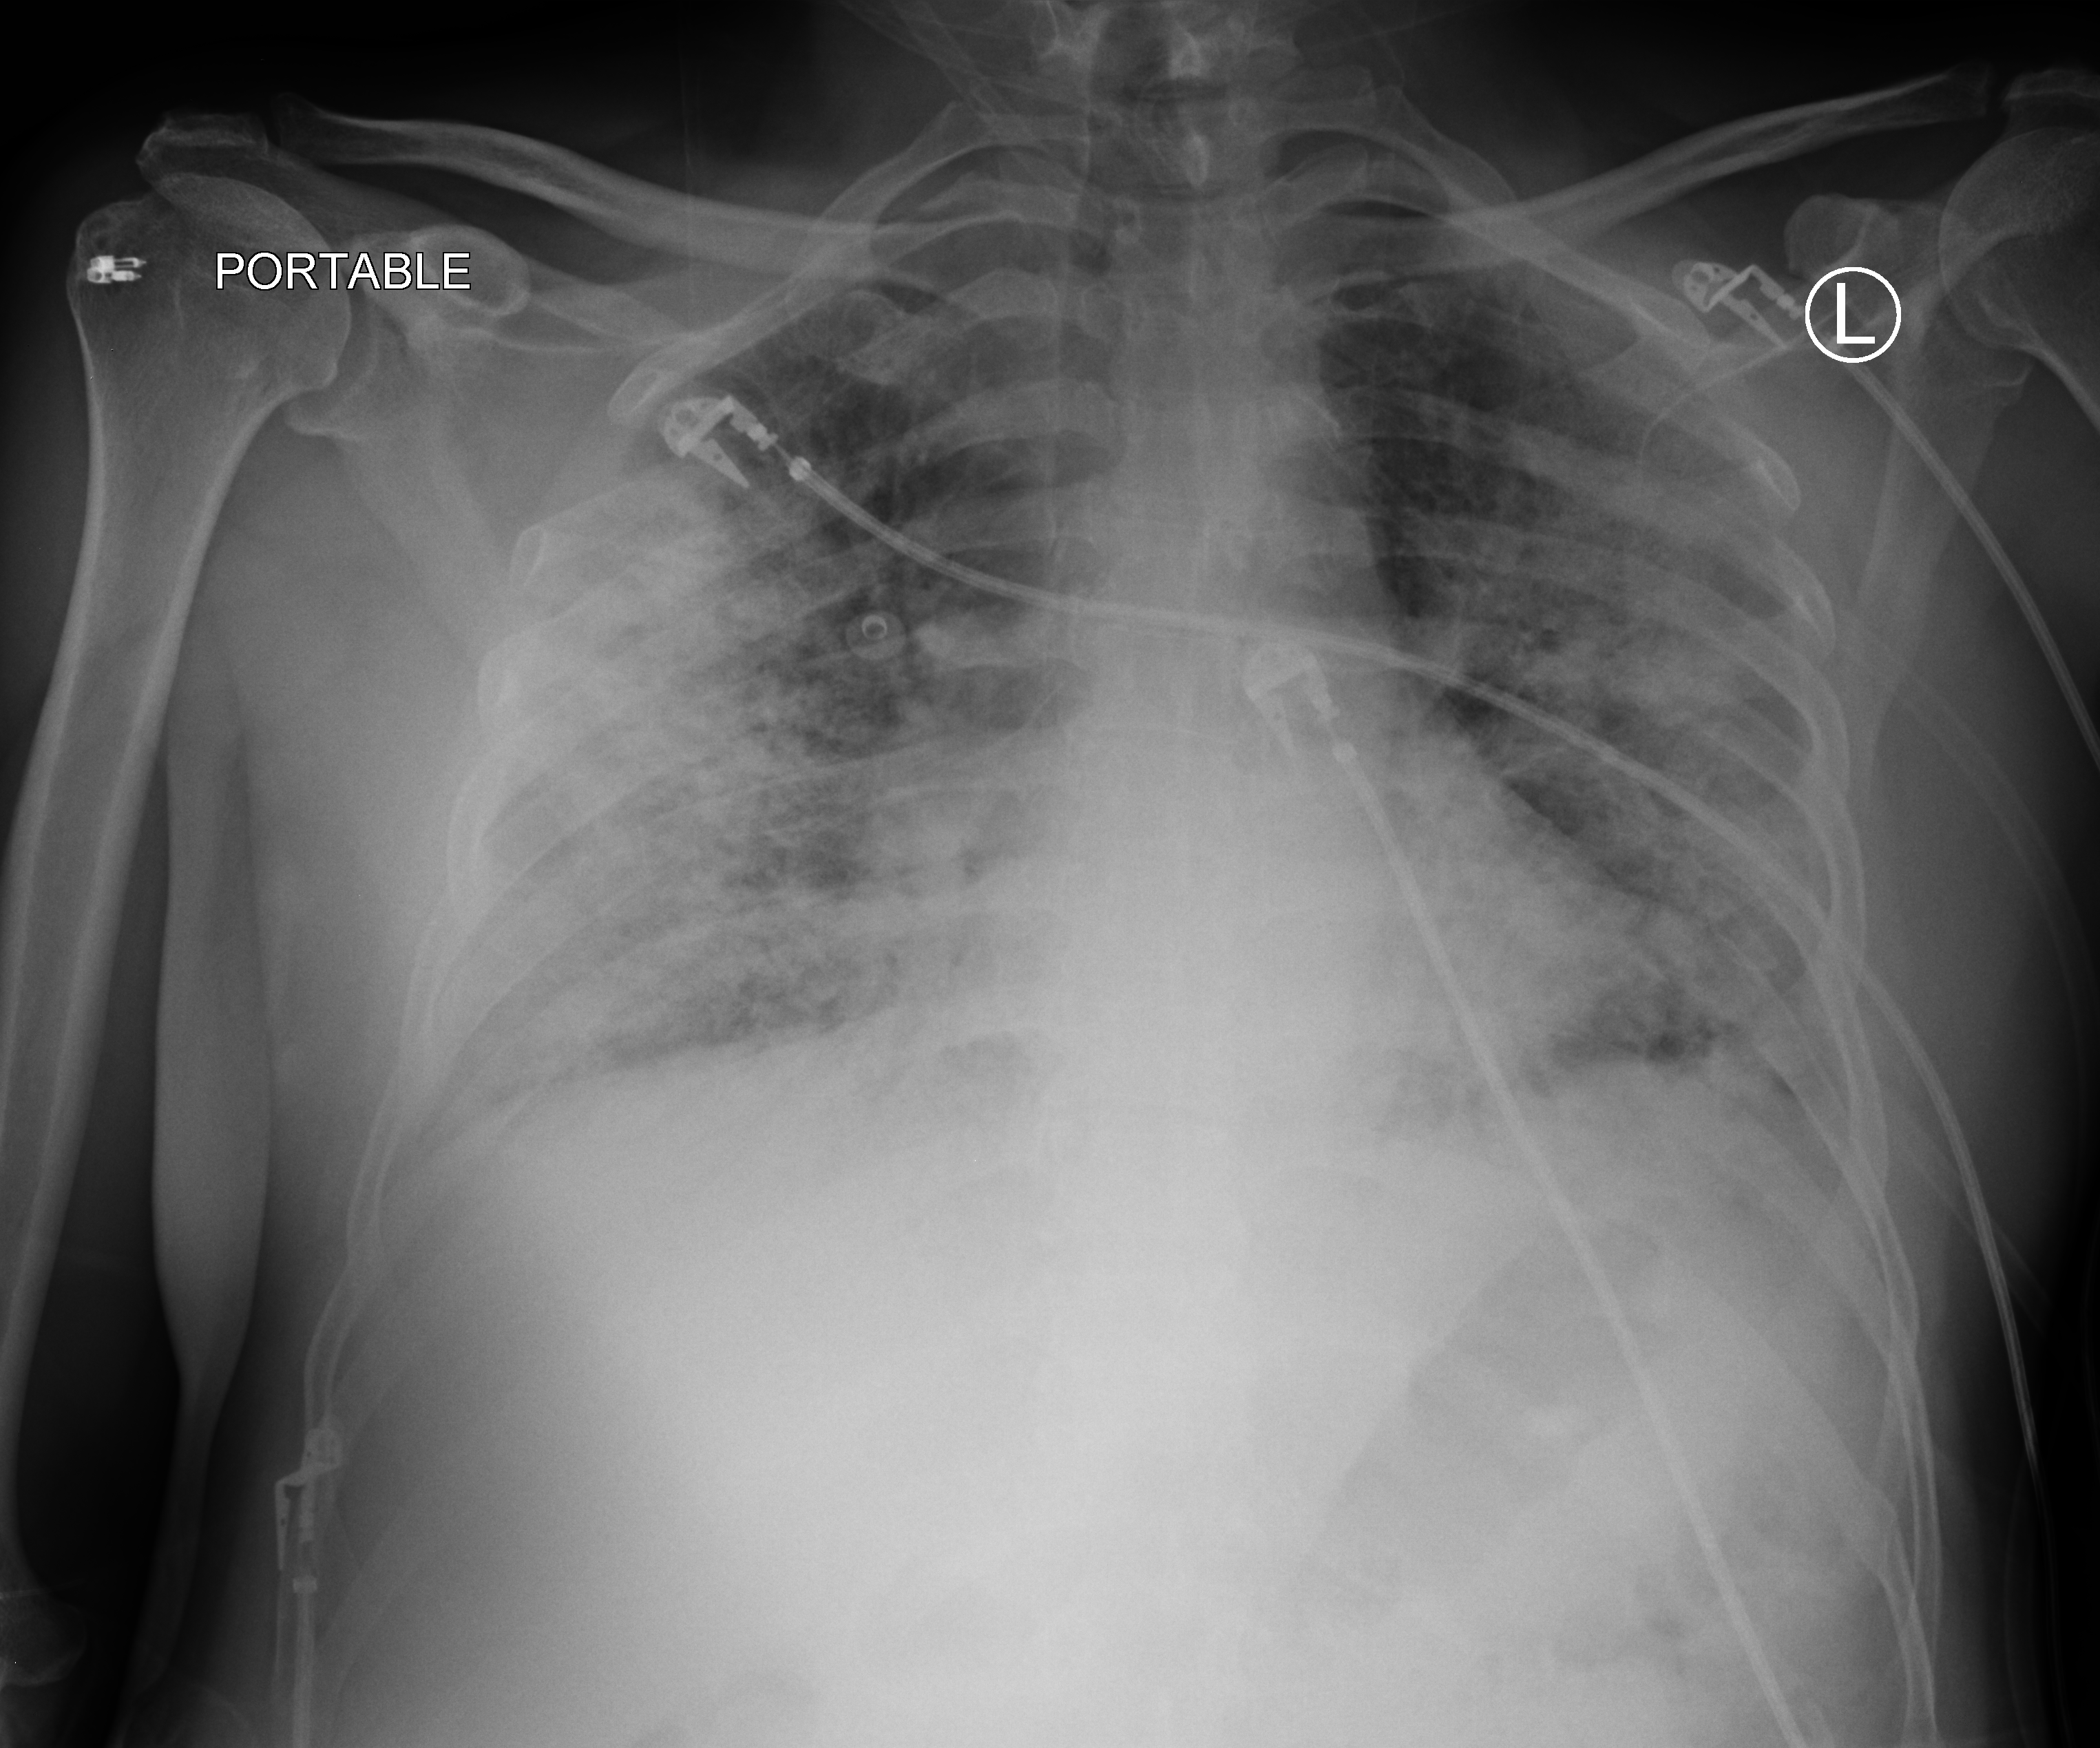
Portable chest radiograph; anteroposterior (AP) projection. Male patient hospitalised with COVID-19, age 60–74 years.
Admission-level facts for this patient (not findings on this image; timing relative to this image not recorded): mechanically ventilated during this hospital stay: yes; chronic kidney disease (admission record): no; hypertension (admission record): no.